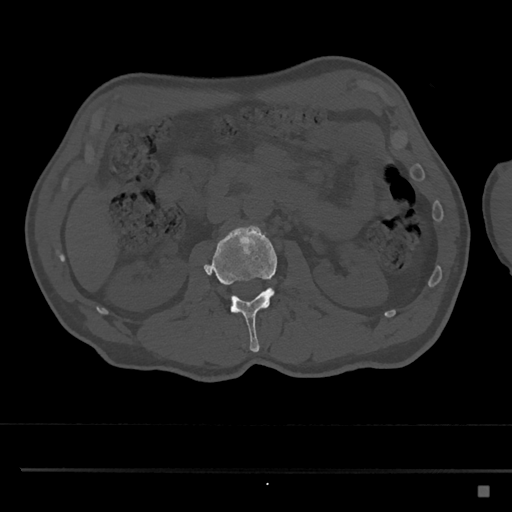
CT including the spine, one axial slice. Slice 751 of 797 in the series (ordered by position). 120 kVp. Bone window (W 1800 / L 400 HU). 0.5 mm slice thickness. 512 × 512 image matrix, field of view 391 × 391 mm. Patient: male, 59 years. Case-level facts recorded for this patient, not image findings: primary cancer: prostate.
Structures marked on this image (semi-automatically segmented with operator editing):
- L2 vertebra: bounding box [x1, y1, x2, y2] px = [203, 226, 278, 352]